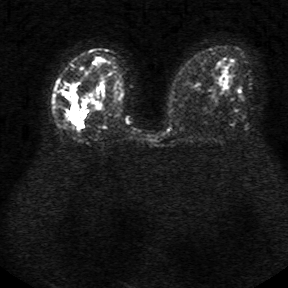
Breast MRI, one axial slice. Position 17 of 34 along the scan axis. Diffusion-weighted series; image 2 of 4 stored at this slice position (different b-values; order by instance number). 1.5 T. 5 mm slice thickness. 288 × 288 image matrix, field of view 340 × 340 mm. Female patient.
Outlined on this slice (outlined manually by an expert reader):
- tumour on diffusion-weighted imaging: bounding box <65,82,88,127> (left, top, right, bottom; pixels)